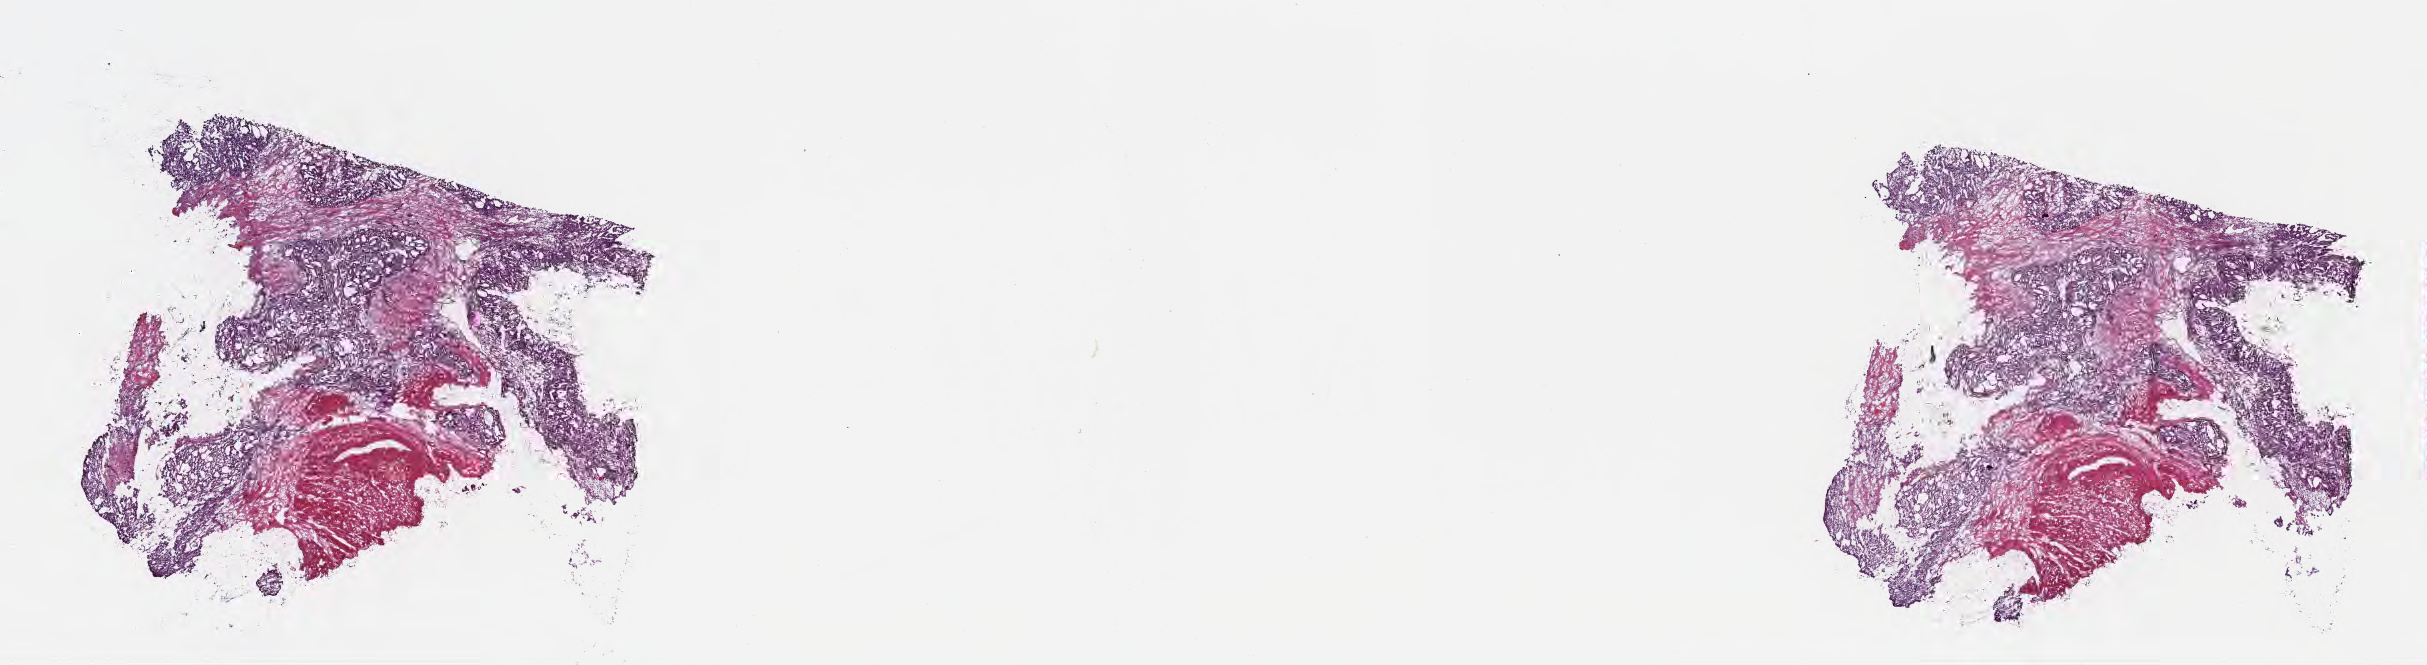
Haematoxylin and eosin whole-slide image, shown as a low-resolution overview of the whole scanned area (about 19.6 x 5.4 mm). Cryosection. Primary tumor. Anatomic site: head of pancreas. Male patient; age at initial diagnosis 72 years. Tumor grade: G2 (moderately differentiated). Composition of this section per pathologist review: tumor cells 59%, tumor nuclei 88%, stromal cells 39%, necrosis 2%, normal cells 0%. Infiltration values recorded for this section: lymphocyte infiltration 7%, monocyte infiltration 1%, neutrophil infiltration 0%.
AJCC pathologic stage: Stage III. Histologic diagnosis: Intraductal papillary mucinous neoplasm with invasive carcinoma.